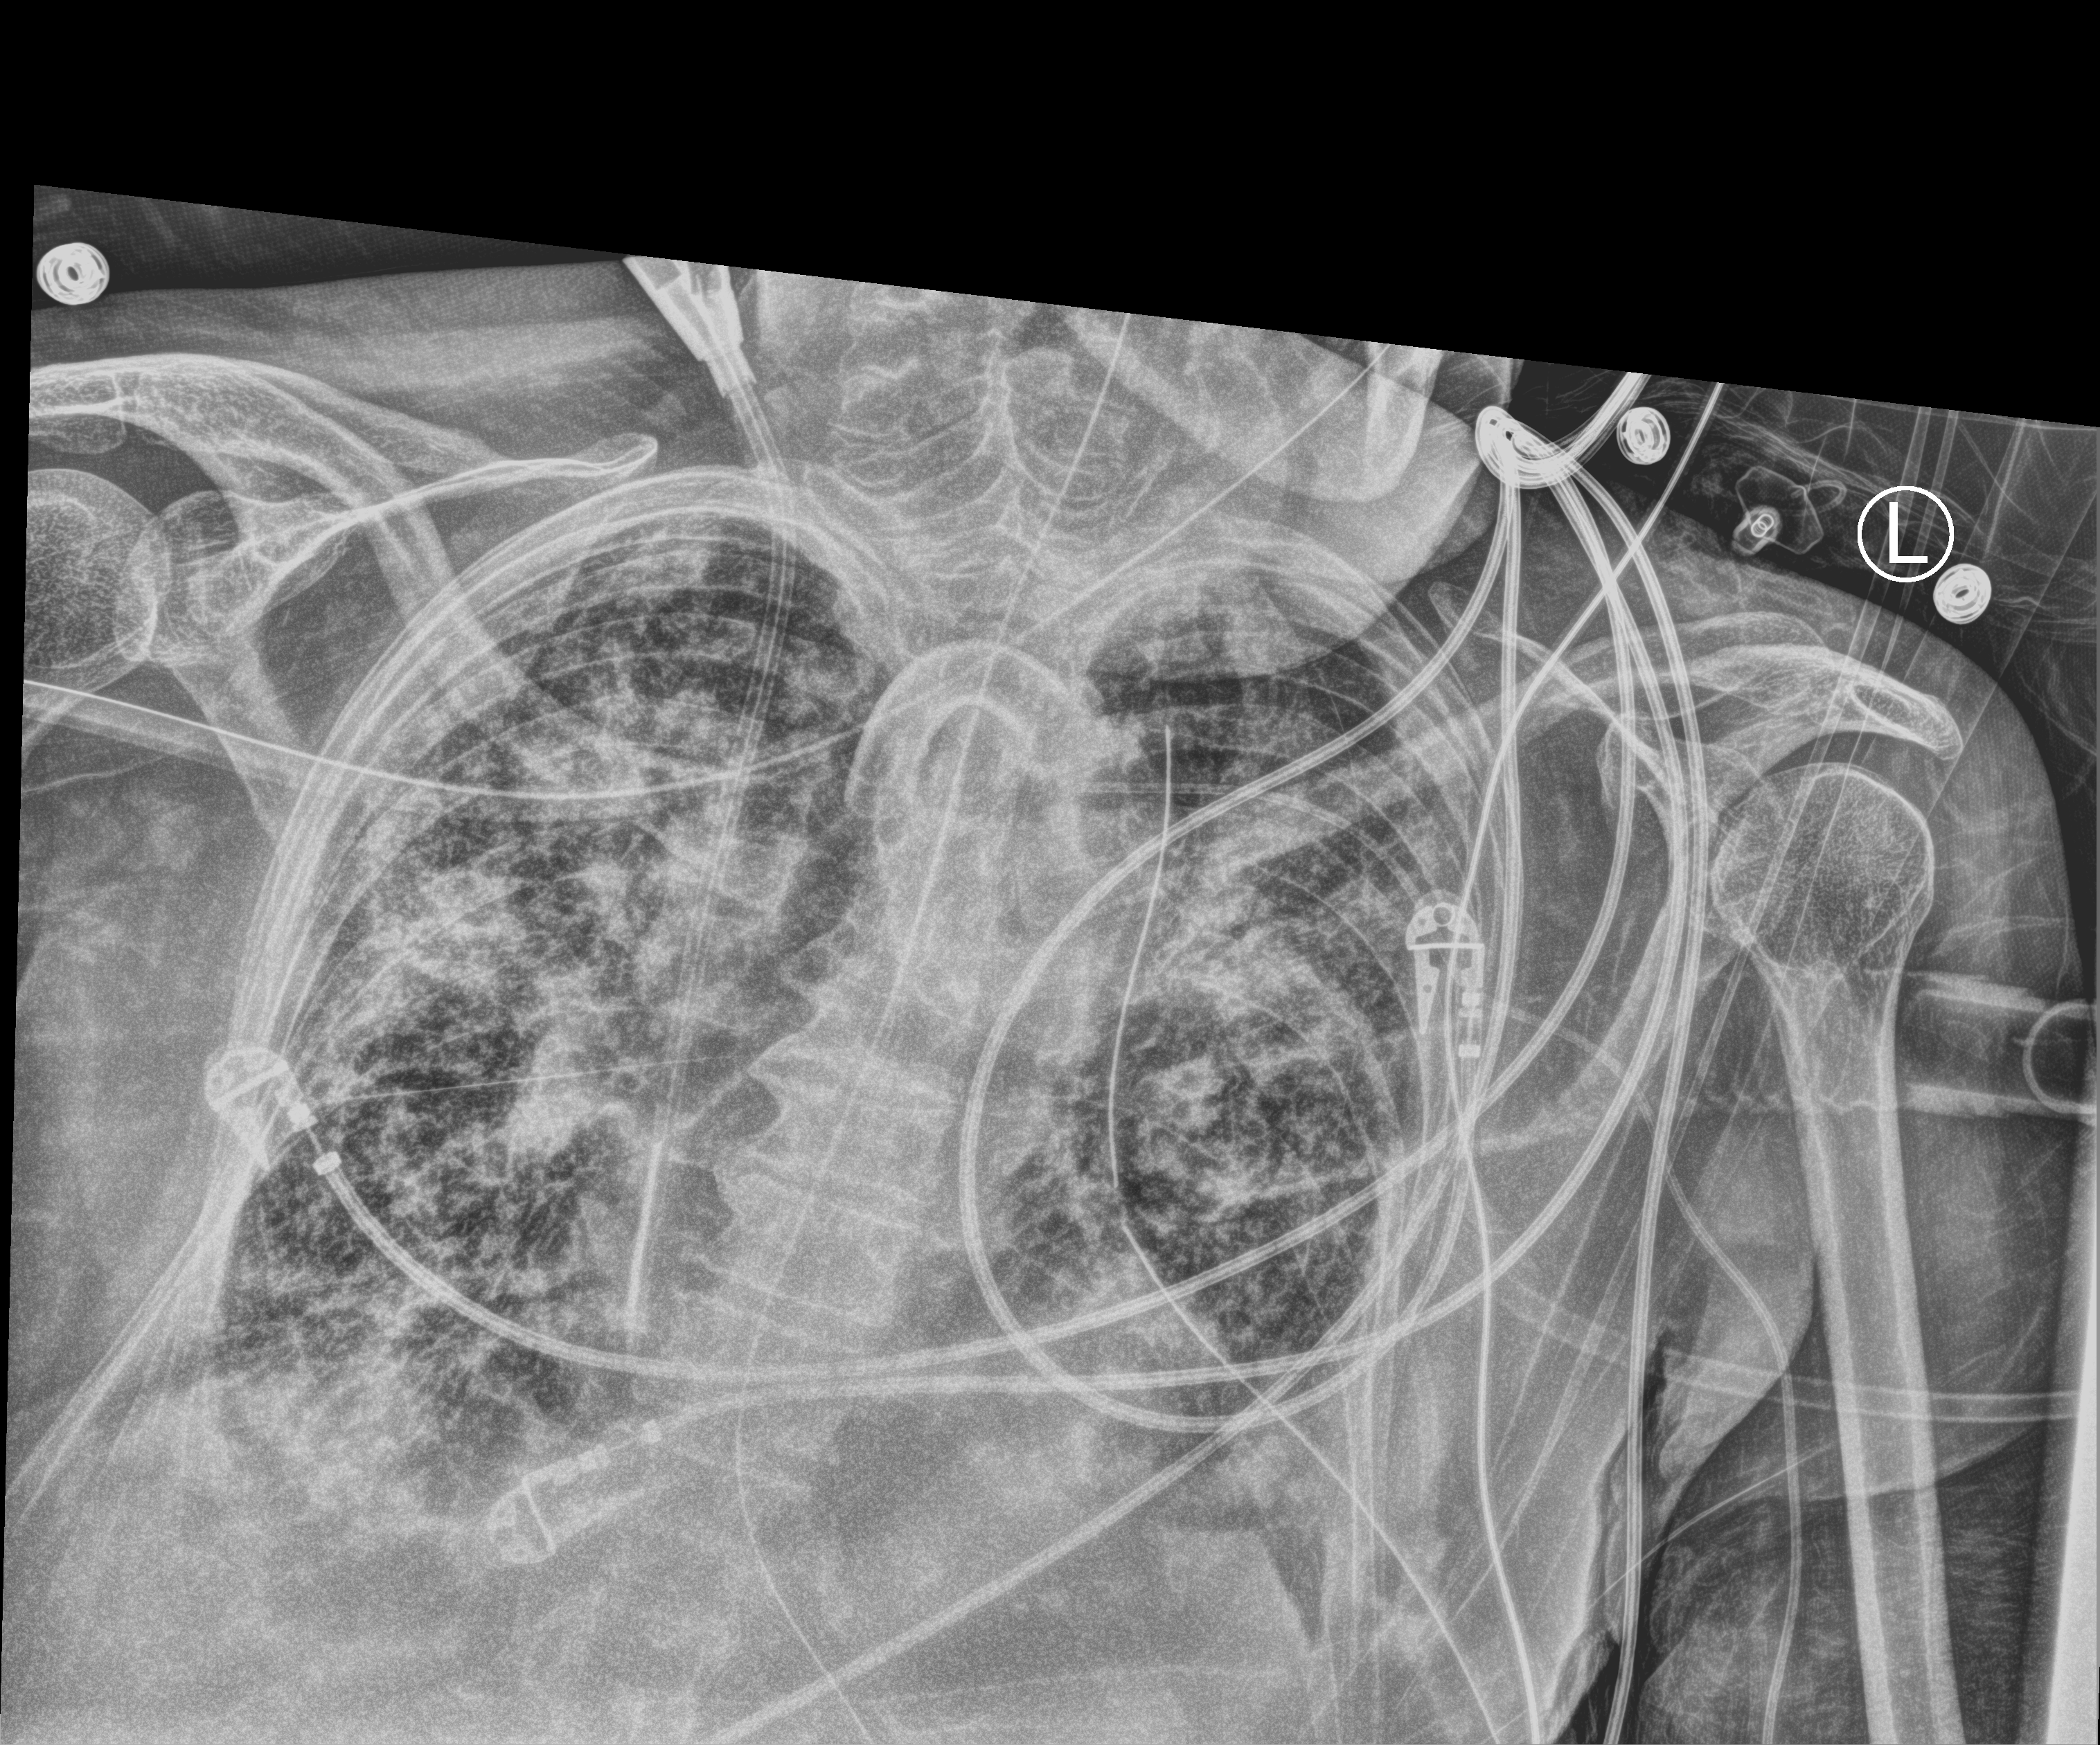
Portable chest radiograph, anteroposterior (AP) projection. Patient hospitalised with COVID-19; female, aged 75–90 years.
Hospital-stay facts (about this admission, not read from this image; timing relative to this image not recorded): mechanically ventilated during this hospital stay: yes; admitted to intensive care during this hospital stay: yes; other chronic lung disease (admission record): yes.